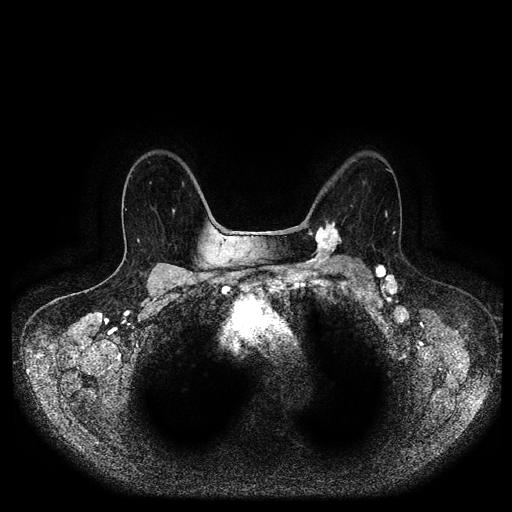
Breast MRI (dynamic contrast-enhanced, multi-phase), one axial slice. Slice 65 of 116 in the series (ordered by position). Dynamic contrast-enhanced series, time point 2 of 5 at this slice position (early post-contrast). 1.5 T. TE 2.6 ms, TR 5.2 ms. 2 mm slice thickness. 512 × 512 image matrix, field of view 380 × 380 mm. Female patient, age 69 years.
Annotated regions visible in this slice (semi-automatic segmentation, software-assisted and operator-edited):
- breast lesion (labelled 'tumour' in the annotation; benign lesions carry a separate 'benign' label): bounding box [x1, y1, x2, y2] px = [304, 216, 344, 269]